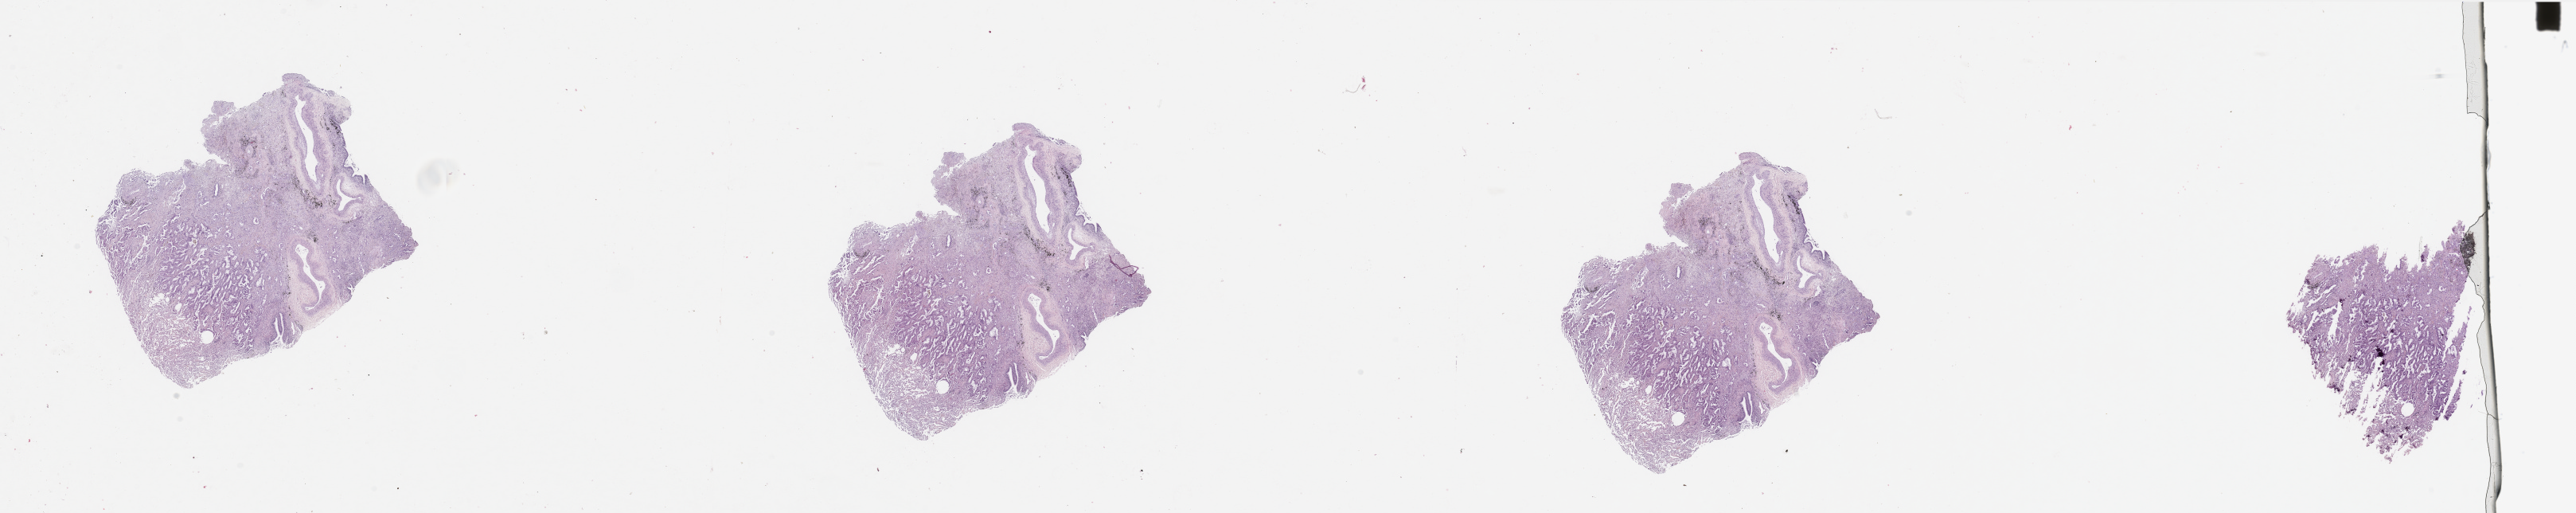
Whole-slide histology image, H&E — shown as a low-resolution overview of the whole scanned area (about 51.2 x 10.2 mm, acquisition: 20x scan), lung, tumour tissue. Patient: male, age 77 years. Histologic grade: G2 (moderately differentiated).
- AJCC pathologic stage: IIIA
- histologic diagnosis: Adenocarcinoma, NOS